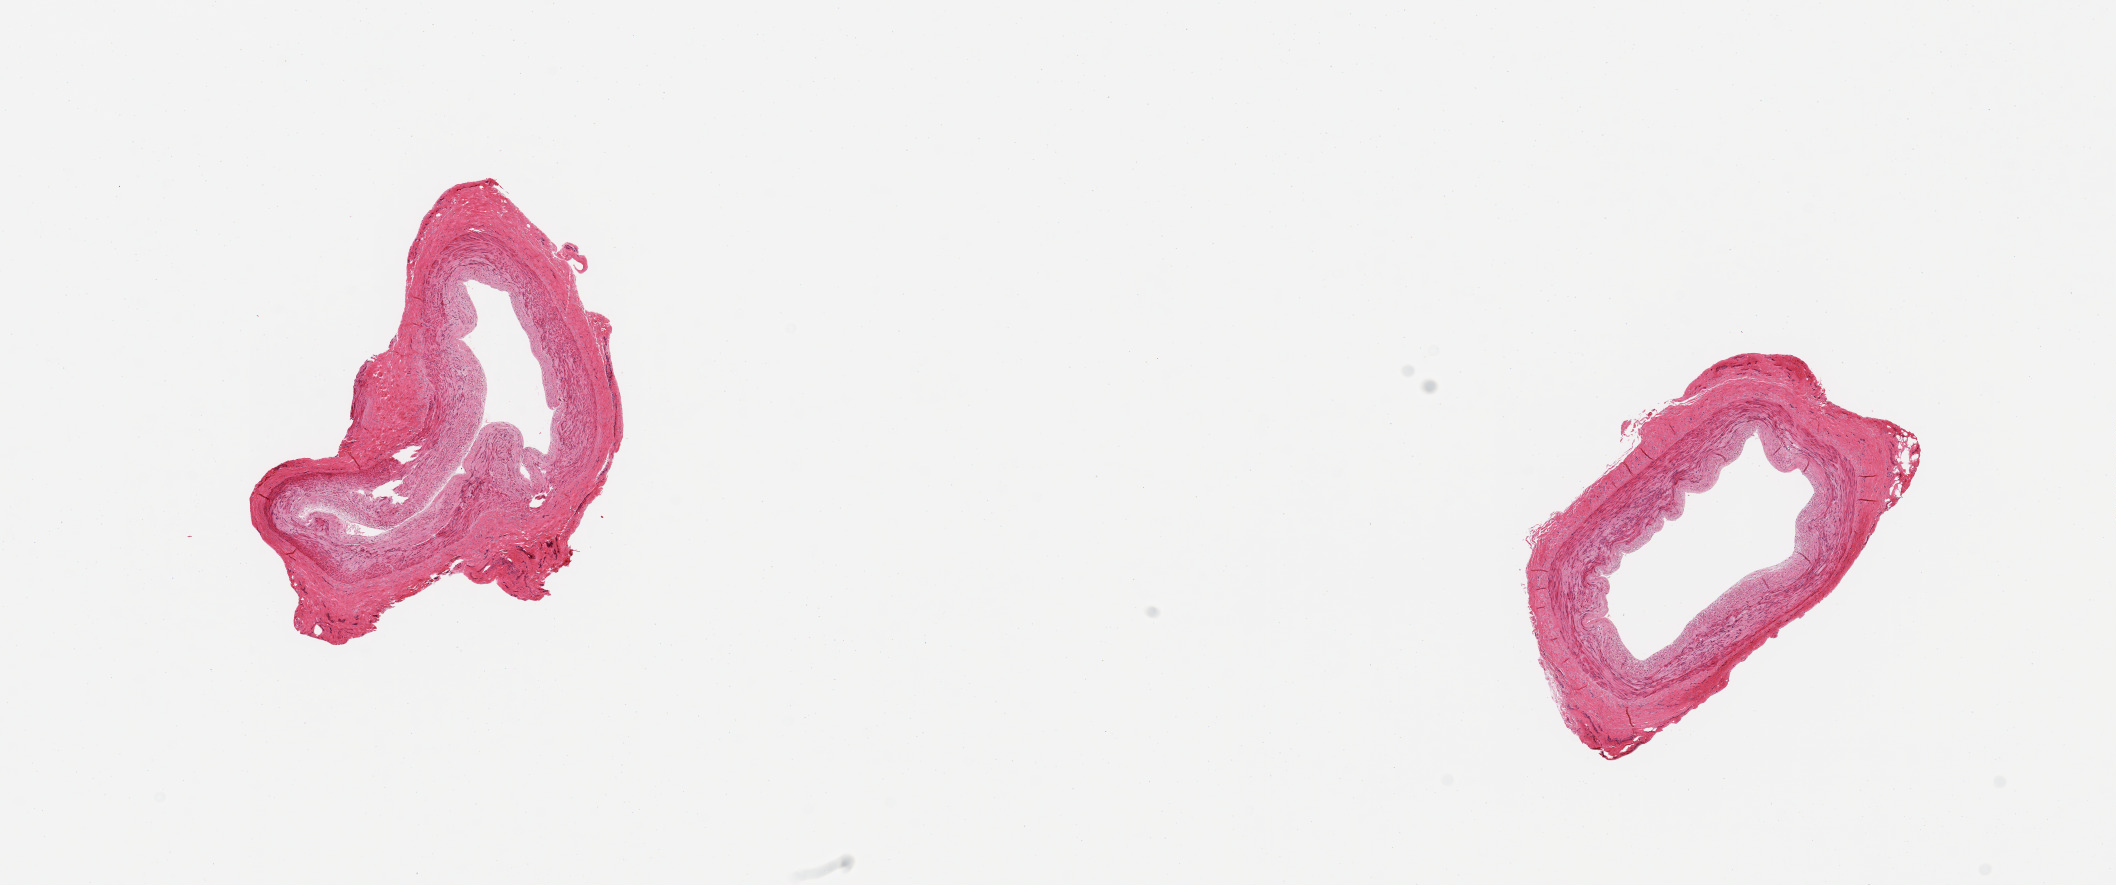
Digitized H&E-stained section — whole scanned area (about 16.7 x 7.0 mm, slide scanned at 20x) shown as a low-resolution overview. PAXgene-fixed paraffin-embedded (PFPE) section. Target tissue: tibial artery. Donor tissue sample. Donor sex: male.
Review note (as recorded): 2 pieces; well trimmed, mild intimal thickening/plaque.